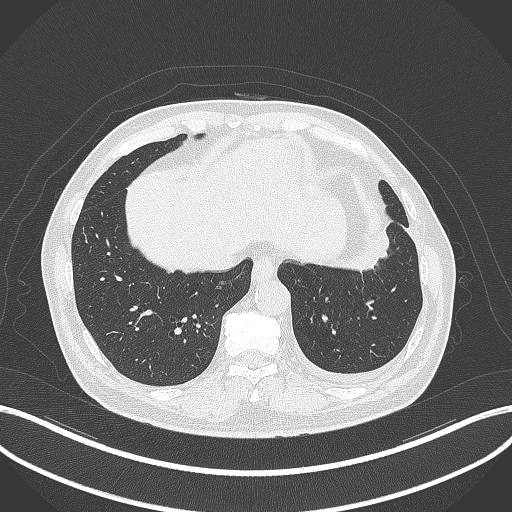
Chest CT, one axial slice. Slice 85 of 230 in the series (ordered by position). Reconstruction kernel B70f. 120 kVp. Lung window (W 1500 / L -600 HU). 512 × 512 image matrix, field of view 400 × 400 mm. Male patient, age 68 years. From the clinical record (not read from this slice): clinical TNM (as recorded): T2b N0 M0.
Structures marked on this image (rectangle marked by the reading radiologist):
- lung tumour (recorded histology: squamous cell carcinoma): bounding box <343,228,397,278> (left, top, right, bottom; pixels)